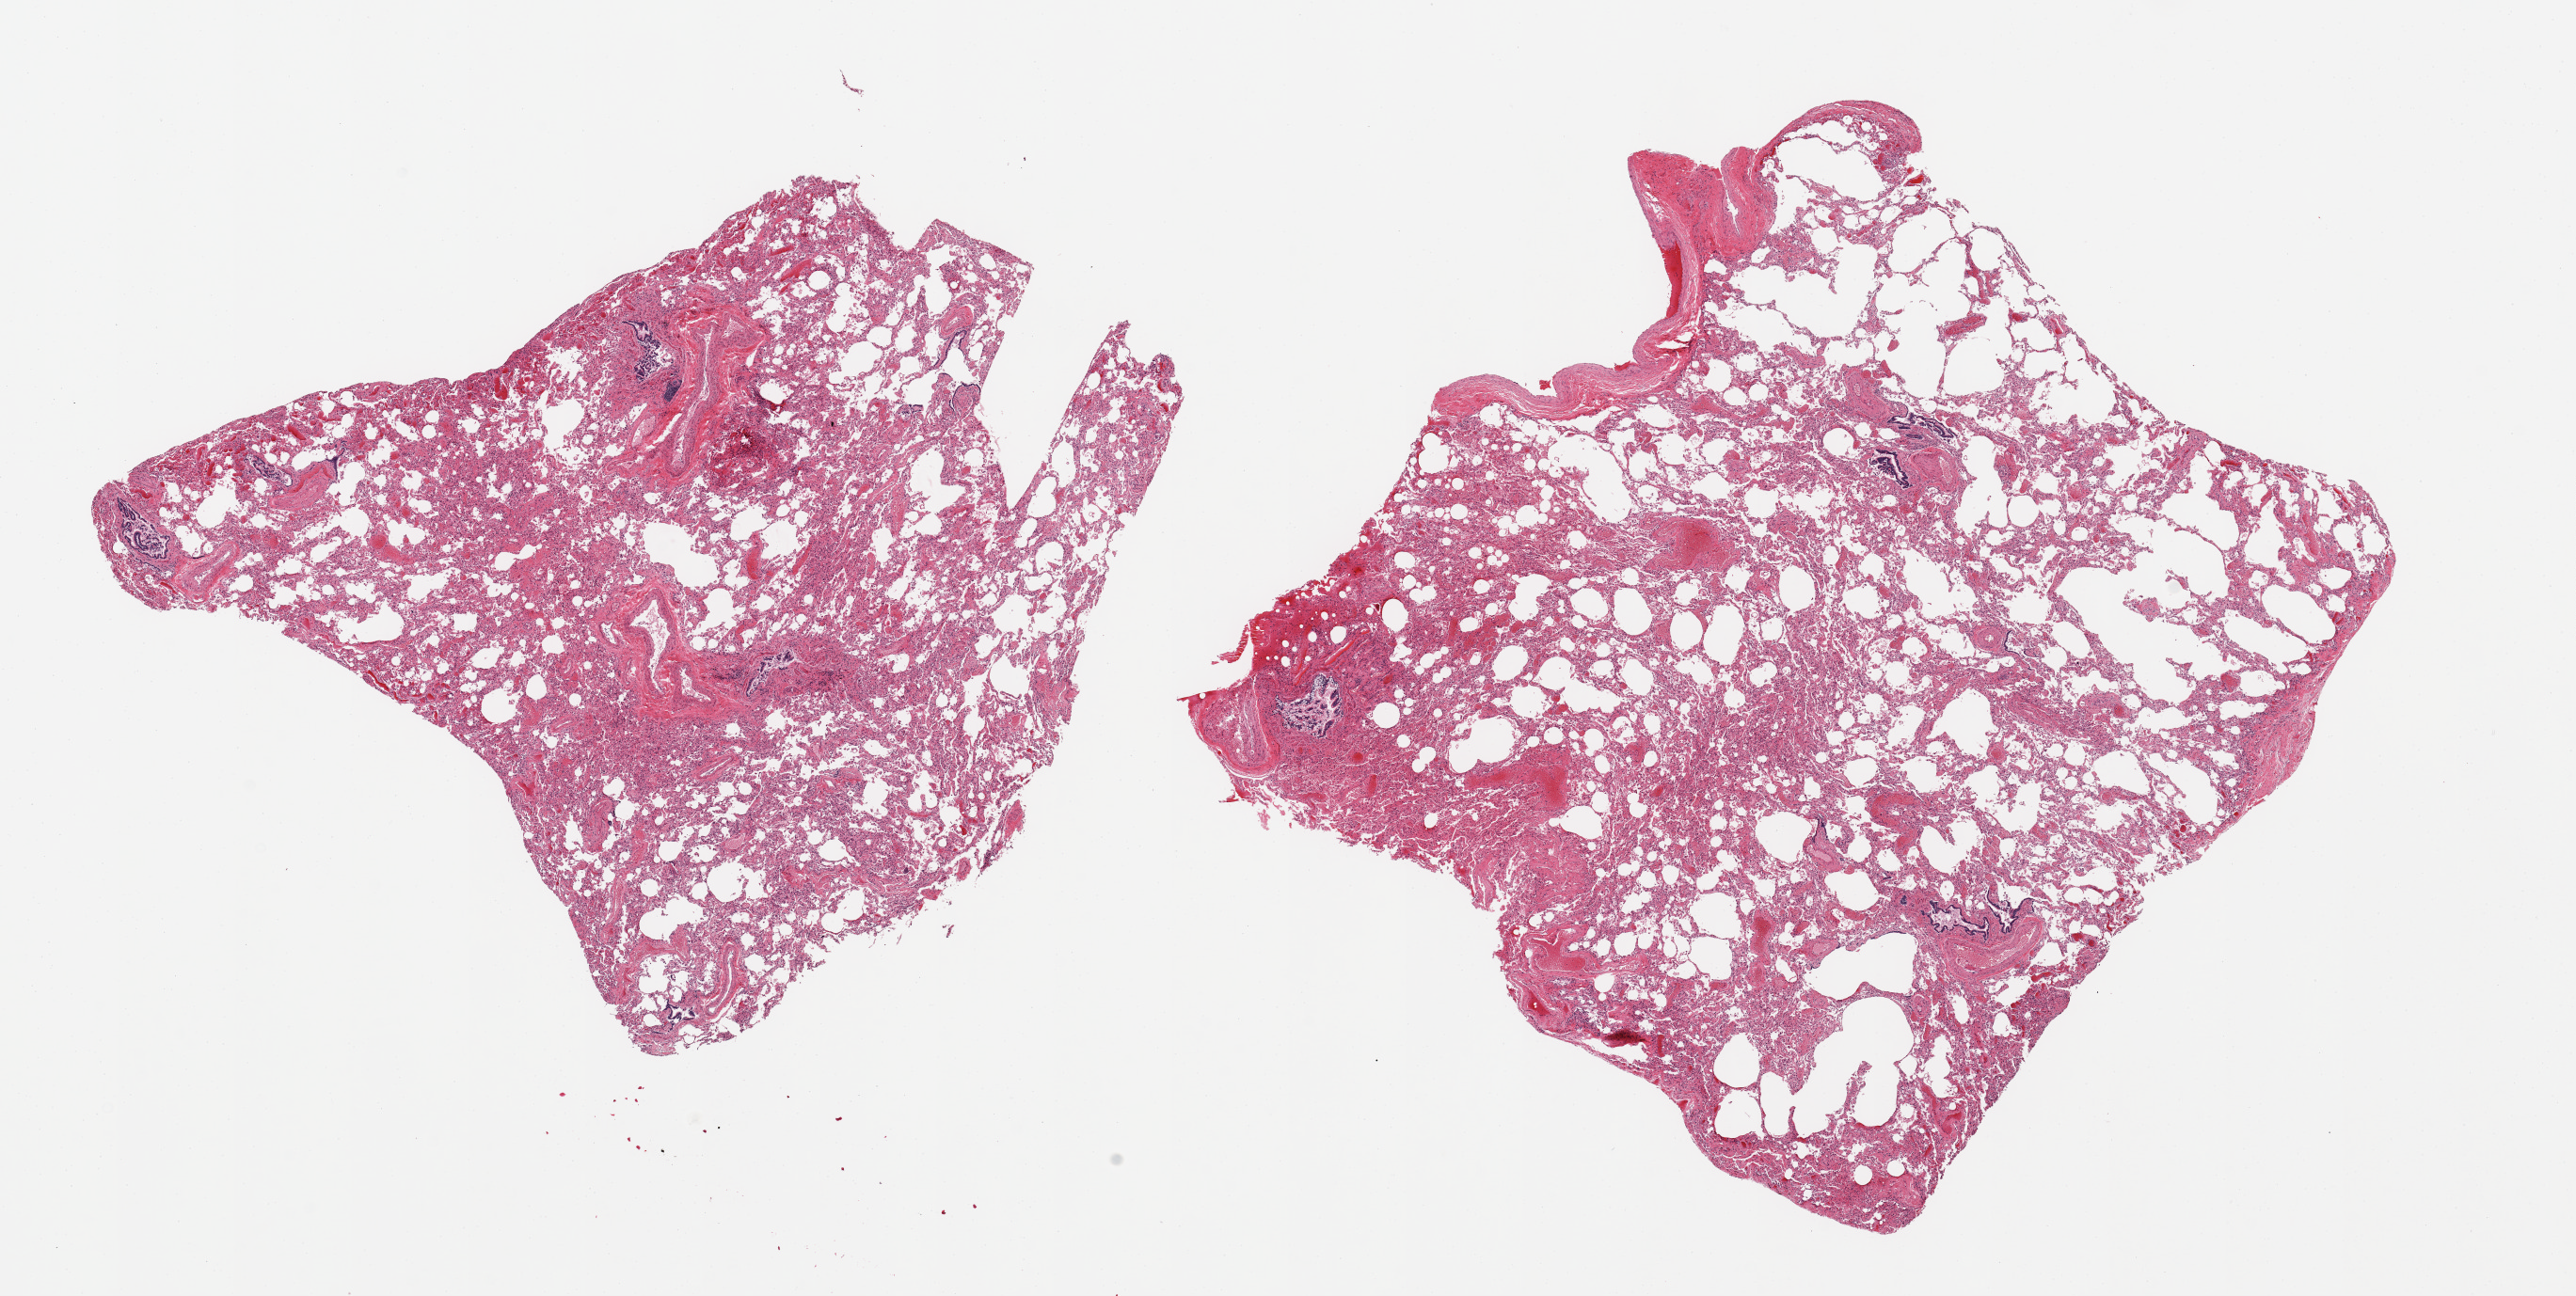
Hematoxylin and eosin (H&E) whole-slide image, low-resolution overview of the scanned area, about 21.7 x 10.9 mm (slide scanned at 20x). PAXgene-fixed paraffin-embedded (PFPE) section. Sampled site (target tissue): lung. Donor tissue sample. Donor sex: male.
Pathologist's review note for this sample: 2 pieces, mild congestion.